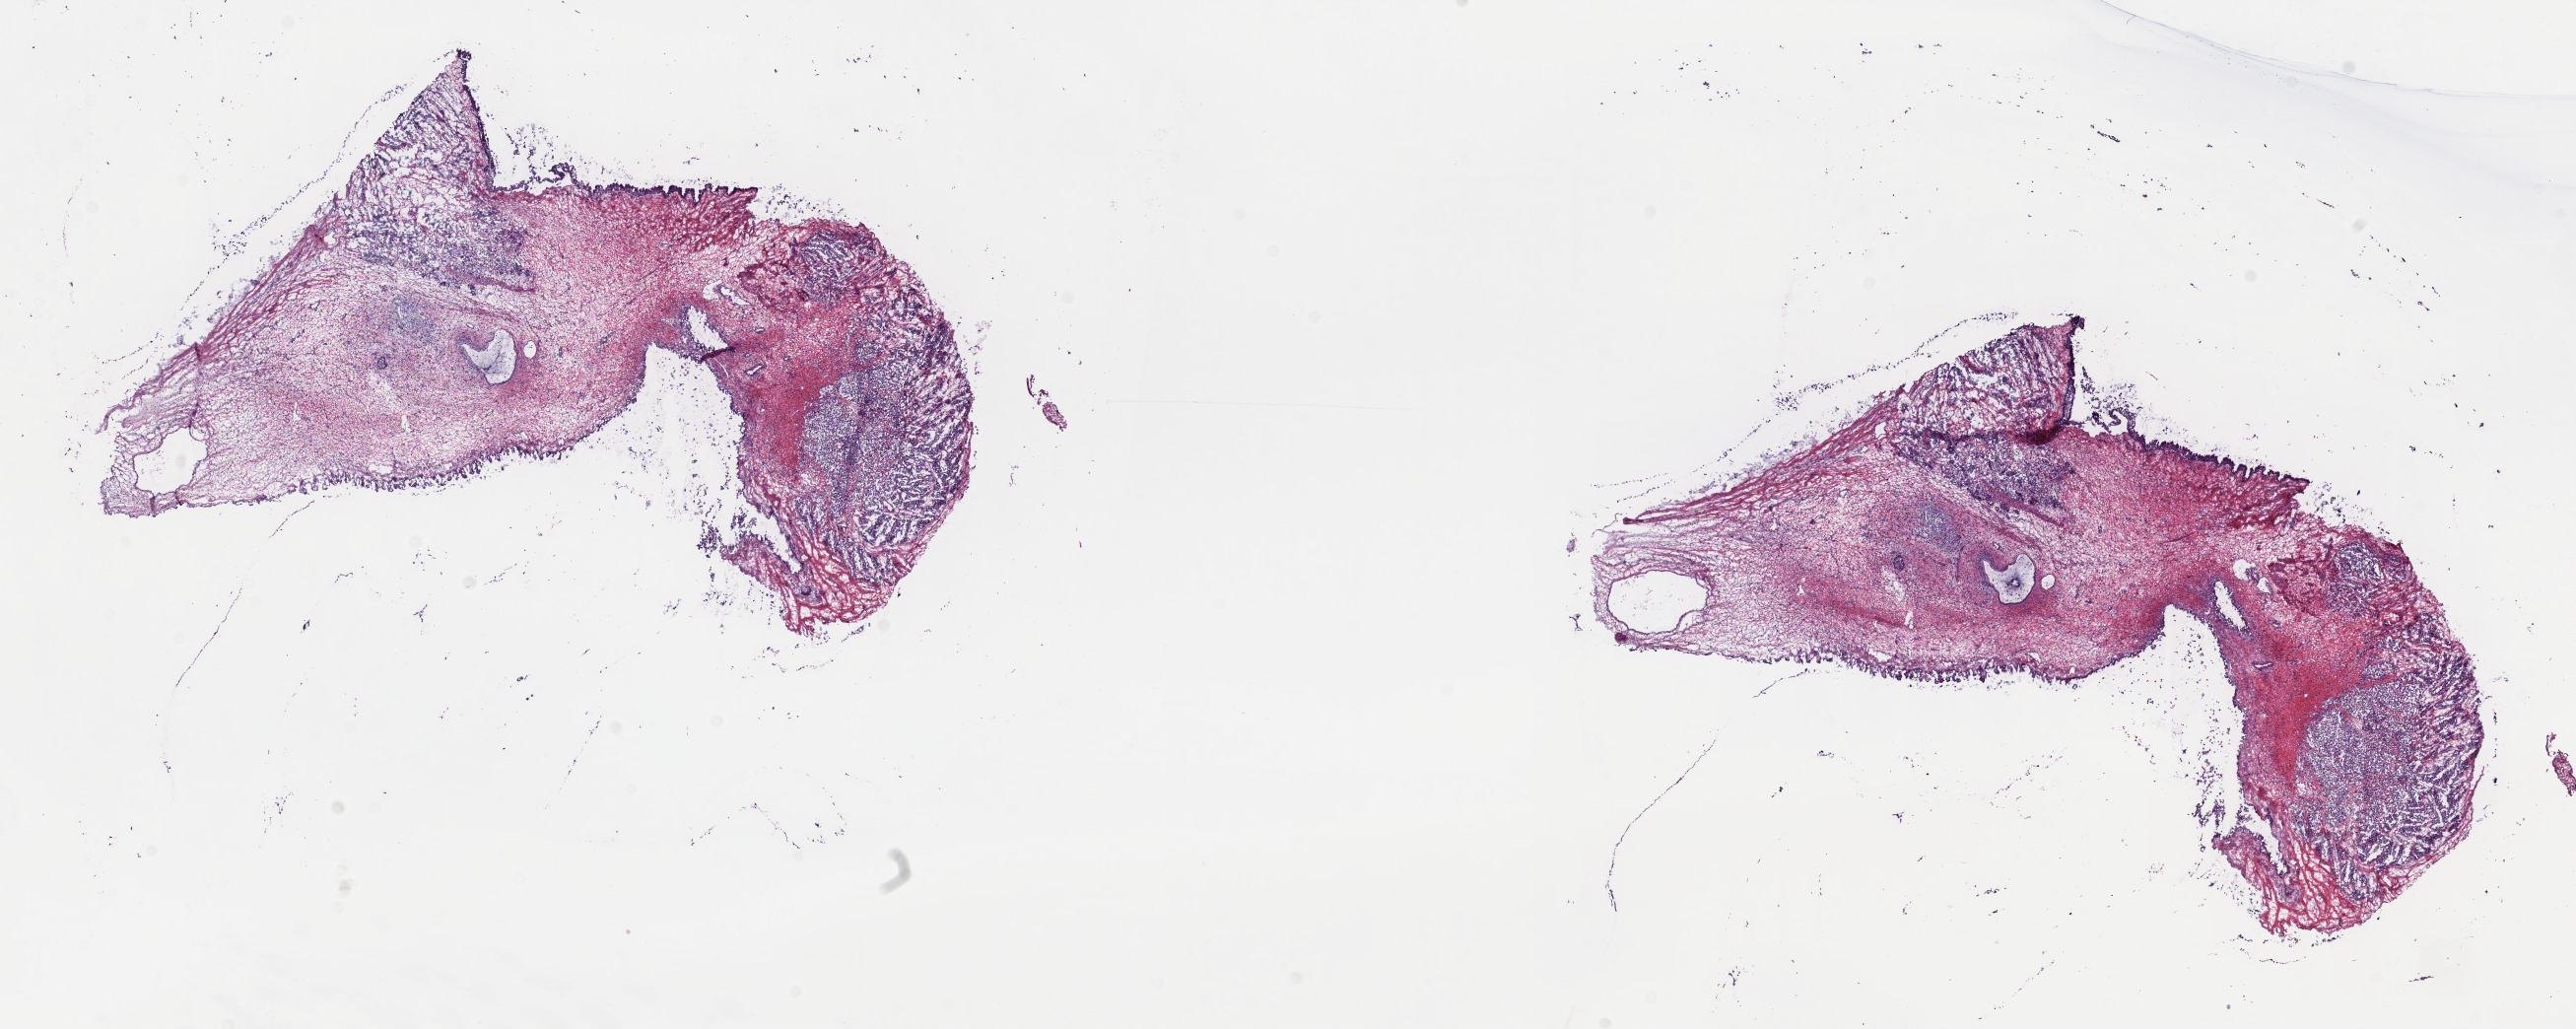
H&E-stained whole-slide image — whole scanned area (about 21.1 x 8.4 mm) shown as a low-resolution overview. Frozen section from the top of the tissue portion. Primary tumour sample from the testis. Patient: male, age at initial diagnosis 53 years. Slide review estimates, as recorded: tumour cells 65%, tumour nuclei 65%, normal cells 0%, stromal cells 35%, necrosis 0%. Inflammatory infiltration, as recorded: lymphocyte infiltration 4%, monocyte infiltration 1%, neutrophil infiltration 2%.
• AJCC pathologic stage: IS (6th edition)
• laterality: bilateral
• diagnosis: Mixed germ cell tumor